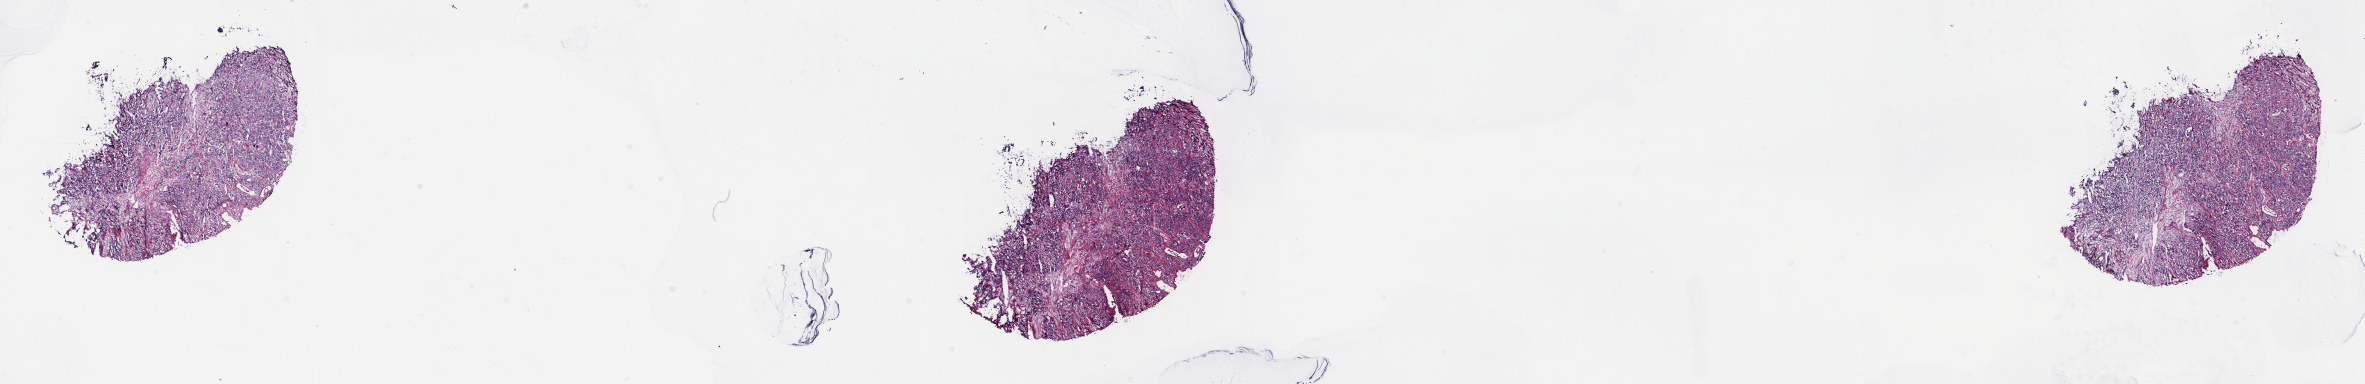
Digitized H&E-stained tissue section (whole slide), whole scanned area (about 38.3 x 6.2 mm, acquisition: 40x scan) shown as a low-resolution overview. Frozen section from the top of the tissue portion. Sample: primary tumour, prostate. Male patient; age at initial diagnosis 66 years. Gleason score: 9 (5+4). Slide review estimates, as recorded: tumour cells 80%, tumour nuclei 90%, normal cells 0%, stromal cells 20%, necrosis 0%. Infiltration values recorded for this section: lymphocyte infiltration 0%, monocyte infiltration 0%, neutrophil infiltration 0%.
Lymph nodes positive (case pathology): 1 of 14 examined. Histologic diagnosis: Adenocarcinoma, NOS (prostate gland).